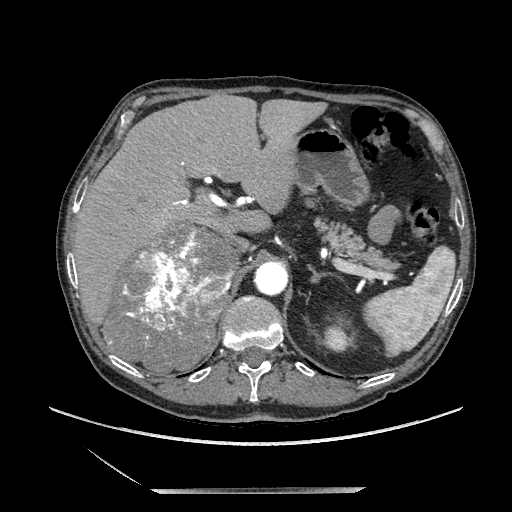
Contrast-enhanced abdominal CT, one axial slice. Slice 144 of 243 in the series (ordered by position). Soft-tissue window (W 400 / L 40 HU). 1.25 mm slice thickness. 512 × 512 image matrix, field of view 420 × 420 mm. Male patient. Case-level facts recorded for this patient, not image findings: diagnosis: adrenocortical carcinoma; tumour side: right adrenal; tumour size at pathology: 16 cm; Ki-67 index: 17 %.
Outlined on this slice (semi-automatic segmentation, software-assisted and operator-edited):
- mass: bounding box [x1, y1, x2, y2] px = [107, 228, 234, 372]